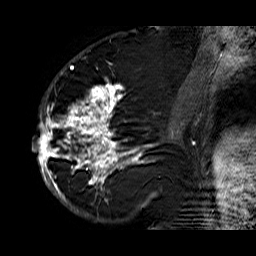
Breast MRI (dynamic contrast-enhanced), one sagittal slice; position 29 of 60 along the scan axis; dynamic contrast-enhanced series, time point 2 of 6 at this slice position (early post-contrast); 1.5 T; TE 6.3 ms, TR 32.9 ms; 256 × 256 image matrix. Female patient. Case-level facts recorded for this patient, not image findings: setting: breast cancer imaged before/during neoadjuvant chemotherapy; receptor status: HR-positive, HER2-negative.
Annotated regions visible in this slice (semi-automatic segmentation, software-assisted and operator-edited):
- analysis volume of interest (the breast-tissue region the enhancement analysis was run in; not a lesion): bounding box [x1, y1, x2, y2] px = [33, 74, 176, 210]
- tumour enhancement mask (voxels above the 100 % enhancement threshold inside the analysis volume of interest): [33, 83, 175, 210]